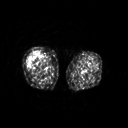
FDG PET of an extremity soft-tissue mass (from a PET/CT study), one axial slice; slice 215 of 311 in the series (ordered by position); 3.27 mm slice thickness; 128 × 128 image matrix. Patient: female, 57 years. From the clinical record (not read from this slice): histological type: pleiomorphic undifferentiated sarcoma; grade: high; site of the primary tumour: right quadricep.
Structures marked on this image (expert contour drawn on MRI and transferred to this co-registered scan by the dataset authors):
- tumour plus oedema (research contour): bounding box [x1, y1, x2, y2] px = [27, 52, 41, 66]